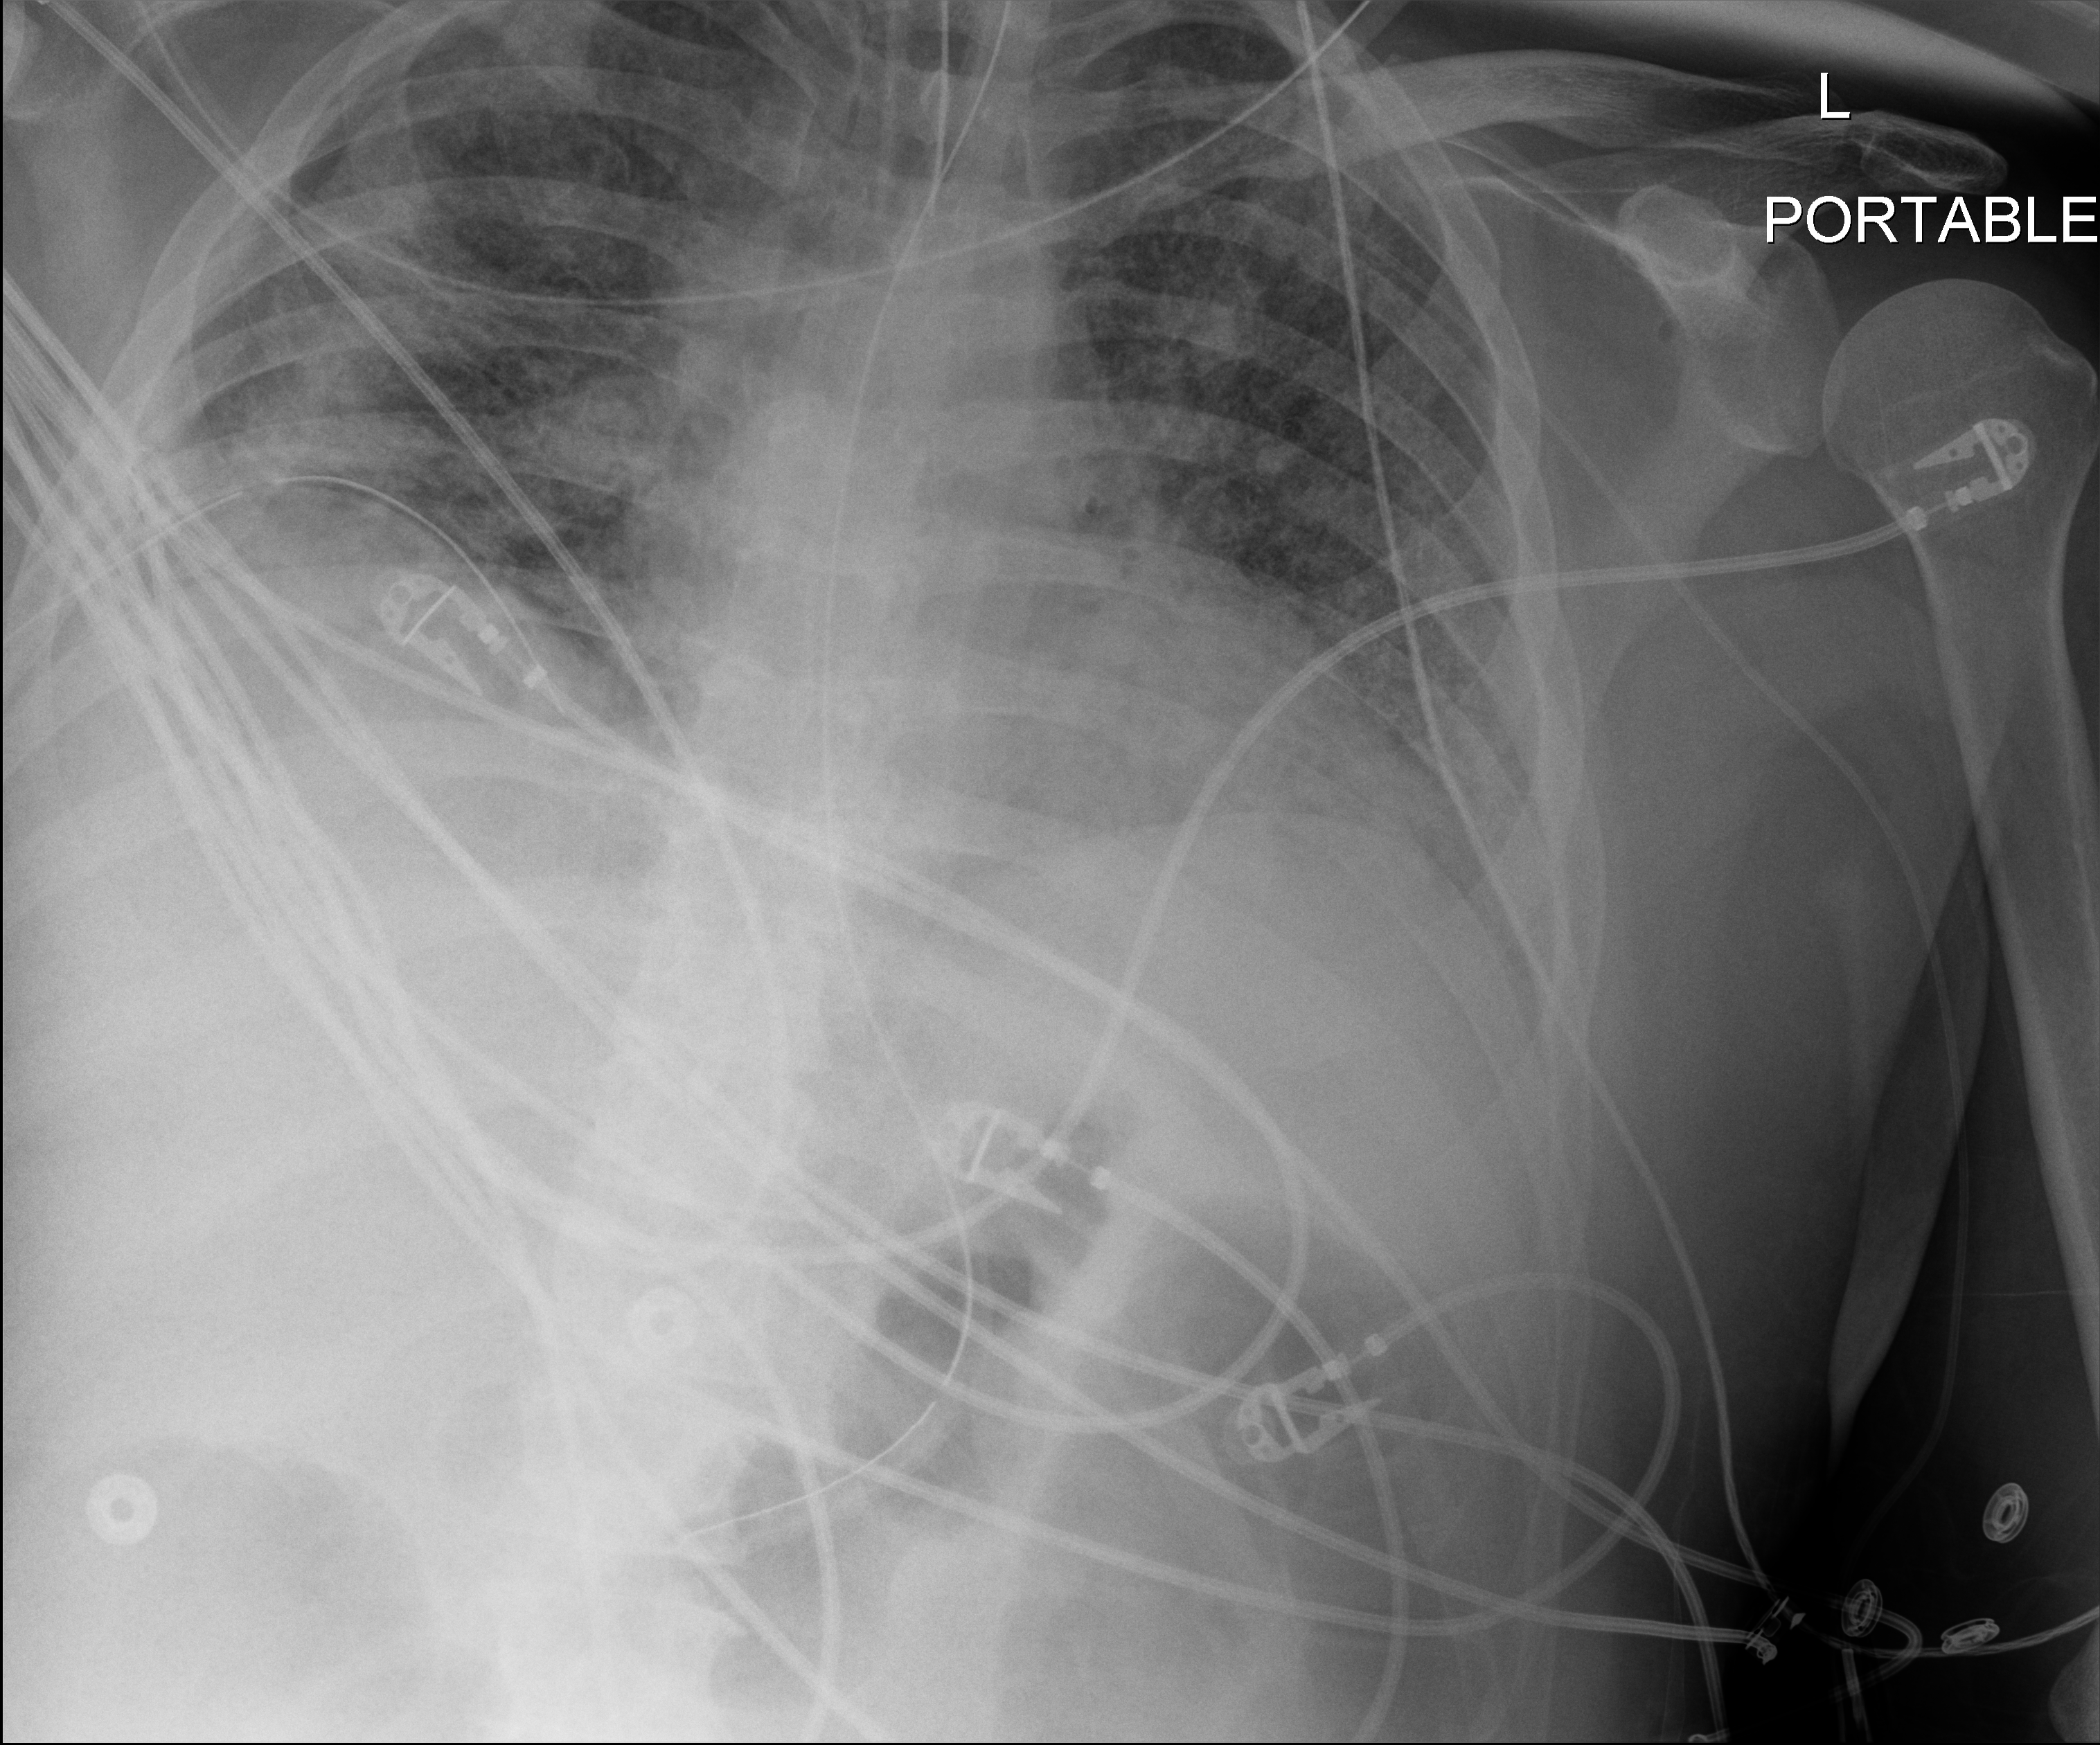
Portable chest radiograph, anteroposterior (AP) projection. Patient hospitalised with COVID-19; male, aged 18–59 years.
Admission-level facts for this patient (not findings on this image; timing relative to this image not recorded):
- smoking status (admission record): never
- length of hospital stay: 80 days
- hypertension (admission record): yes